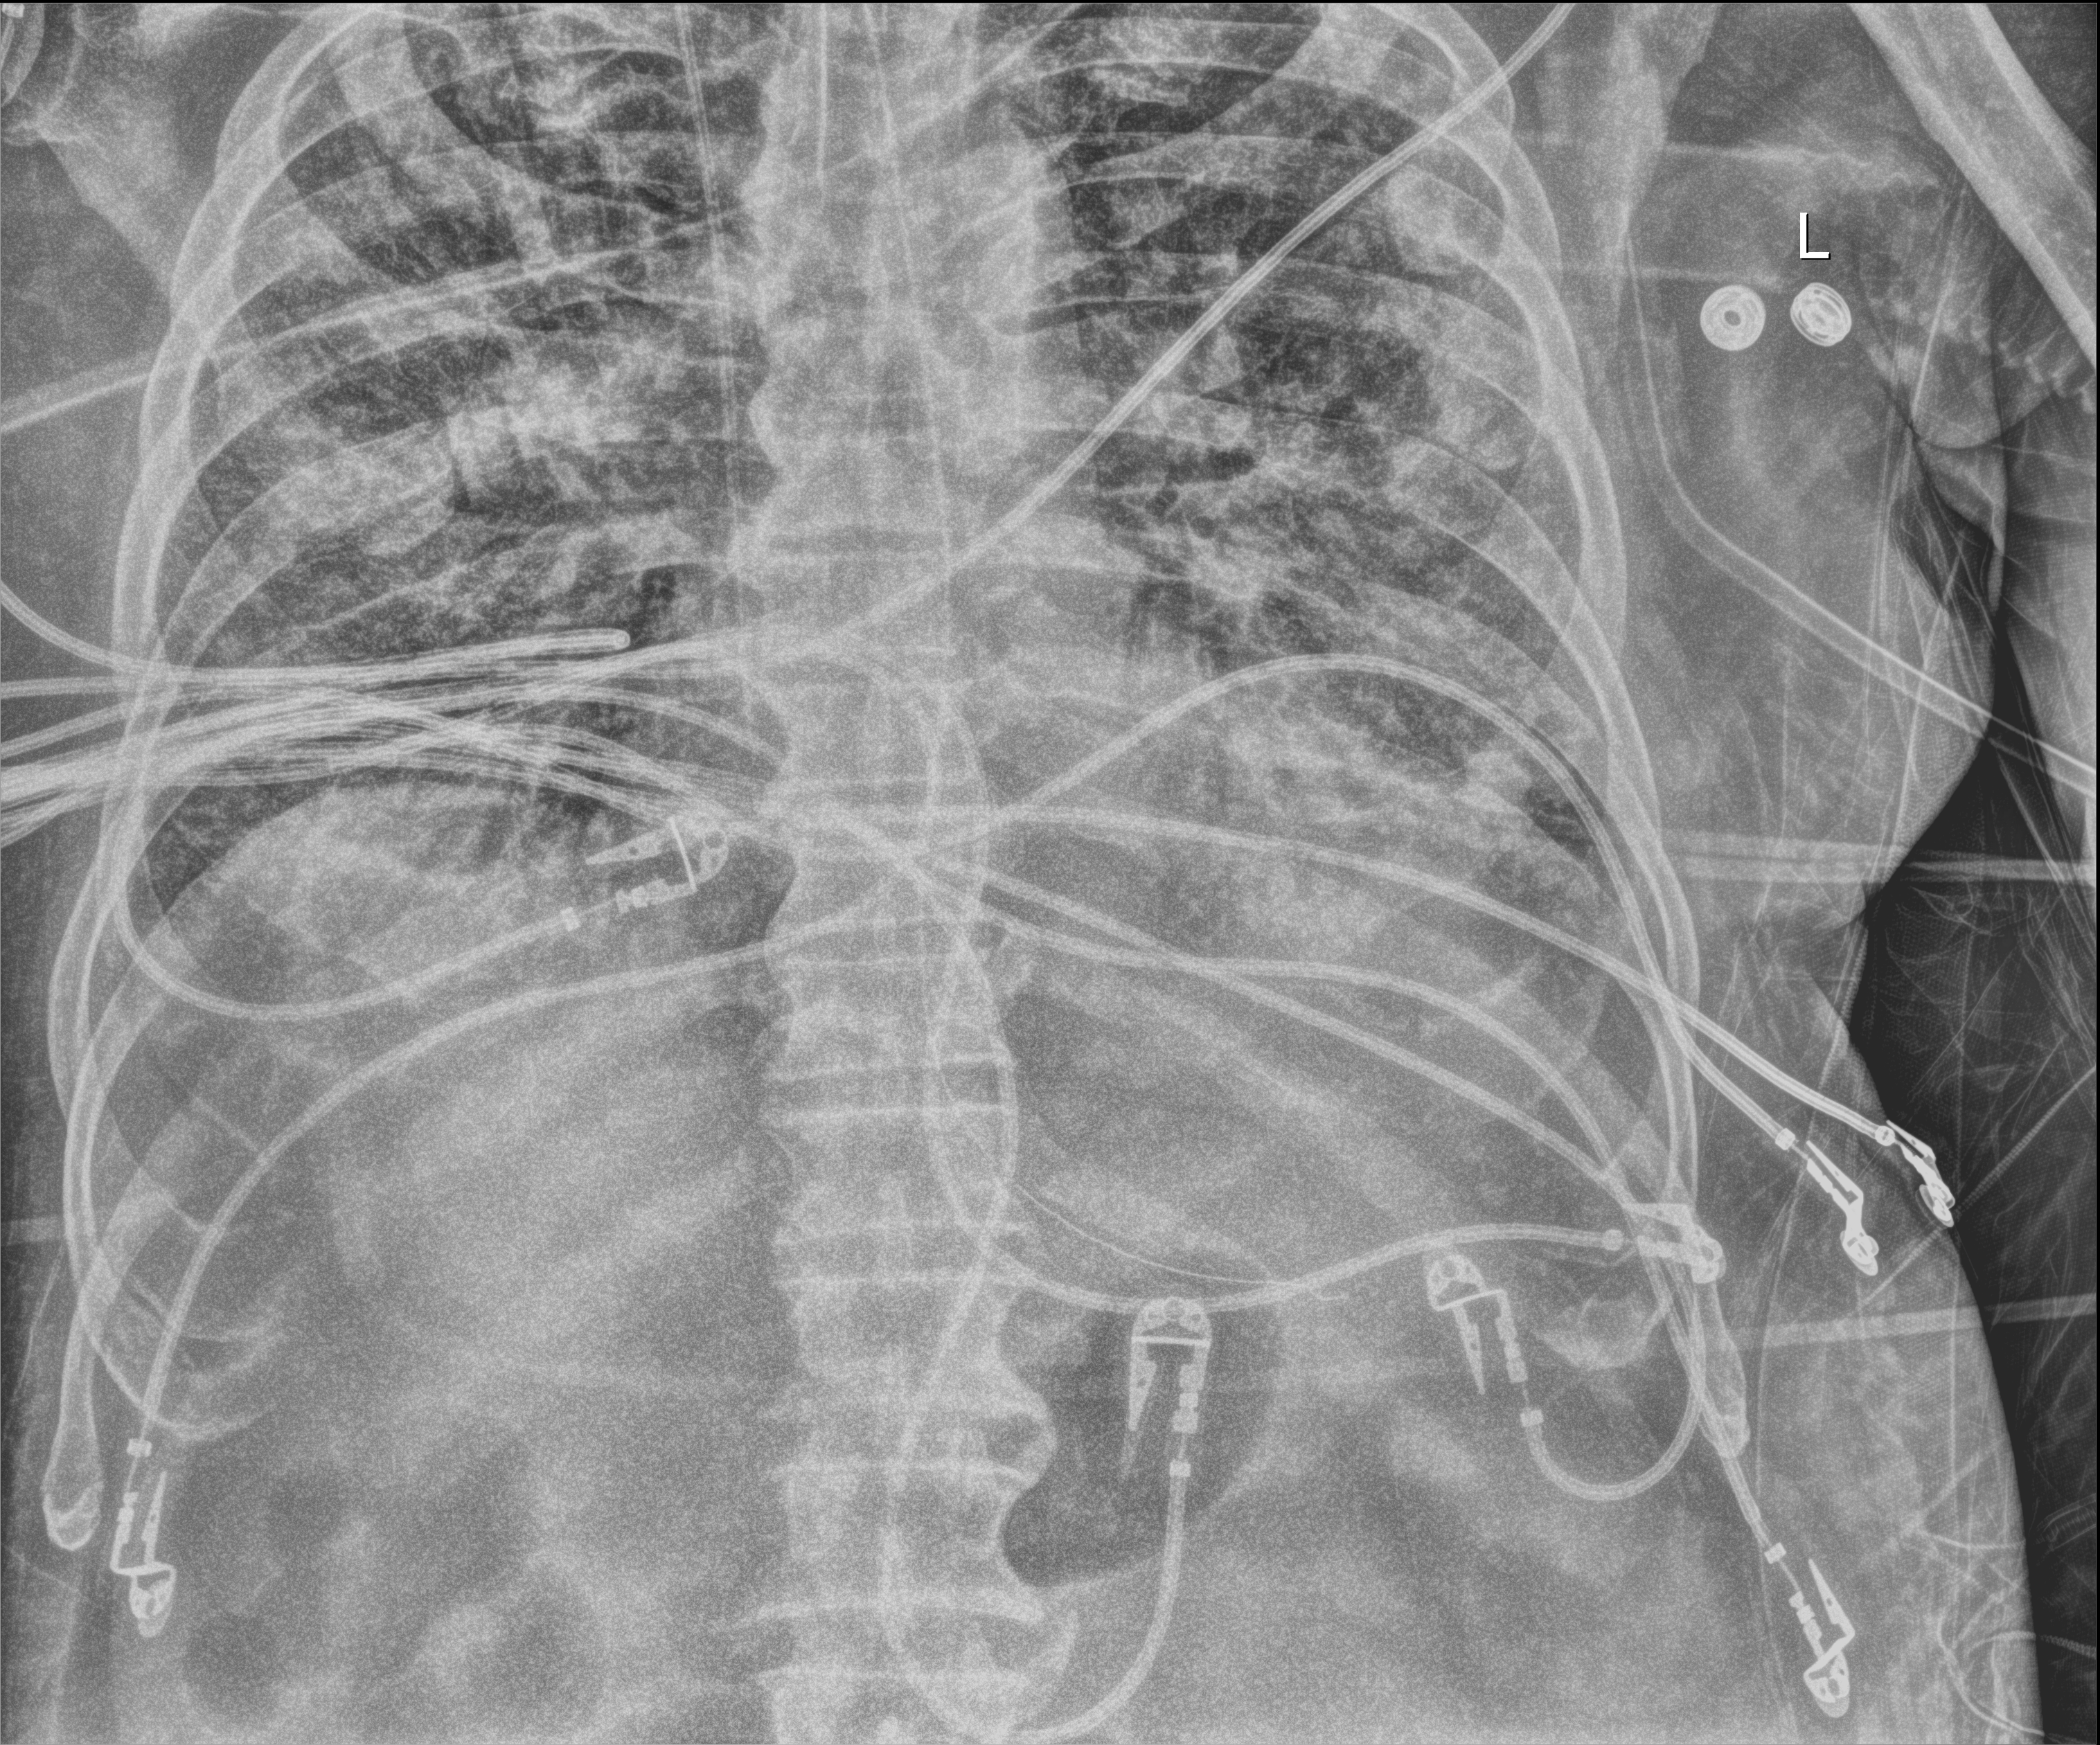
Chest X-ray (portable); anteroposterior (AP) projection. Male patient hospitalised with COVID-19, age 75–90 years.
From the hospital-stay record, not from the radiograph (when in the stay this image was taken is not recorded):
- mechanically ventilated during this hospital stay: yes
- COPD (admission record): no